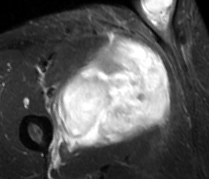
MRI of an extremity soft-tissue mass, one axial slice. STIR. MR volume resampled by the dataset authors to the PET/CT grid (not the native acquisition matrix). 3.27 mm slice thickness. 209 × 179 image matrix, field of view 204 × 175 mm. Male patient. Case-level facts recorded for this patient, not image findings: histological type: undifferentiated - pleiomorphic; grade: high; site of the primary tumour: right thigh.
Outlined on this slice (expert contour drawn on MRI and transferred to this co-registered scan by the dataset authors):
- gross tumour volume including surrounding oedema: box from (x=51, y=37) to (x=170, y=150) px
- gross tumour volume (mass): (x=59, y=37)–(x=170, y=149)